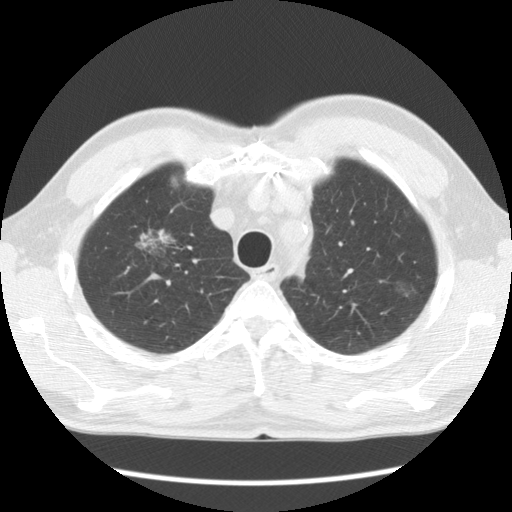
Low-dose screening chest CT, axial slice; baseline annual screen; lung window (W 1500 / L -600 HU); 2.5 mm slice thickness; slice 23 of 132 in the series; 512 × 512 image matrix, field of view 340 × 340 mm. Male, age 64 years at enrolment. Former smoker at enrolment.
• Lesion marked by an expert reader, bounding box <97,196,178,274> (left, top, right, bottom; pixels).
• The screening reader recorded 2 non-calcified nodules or masses ≥4 mm on this exam; which of them this box marks is not recorded.
• Official screen result: positive, change unspecified: nodule(s) >= 4 mm or enlarging nodule(s), mass(es), or other non-specific abnormalities suspicious for lung cancer.
• Participant outcome: lung cancer diagnosed 750 days after this screen — adenocarcinoma, NOS, right upper lobe, well differentiated (G1), stage IB (AJCC 6th edition), 45 mm at pathology.